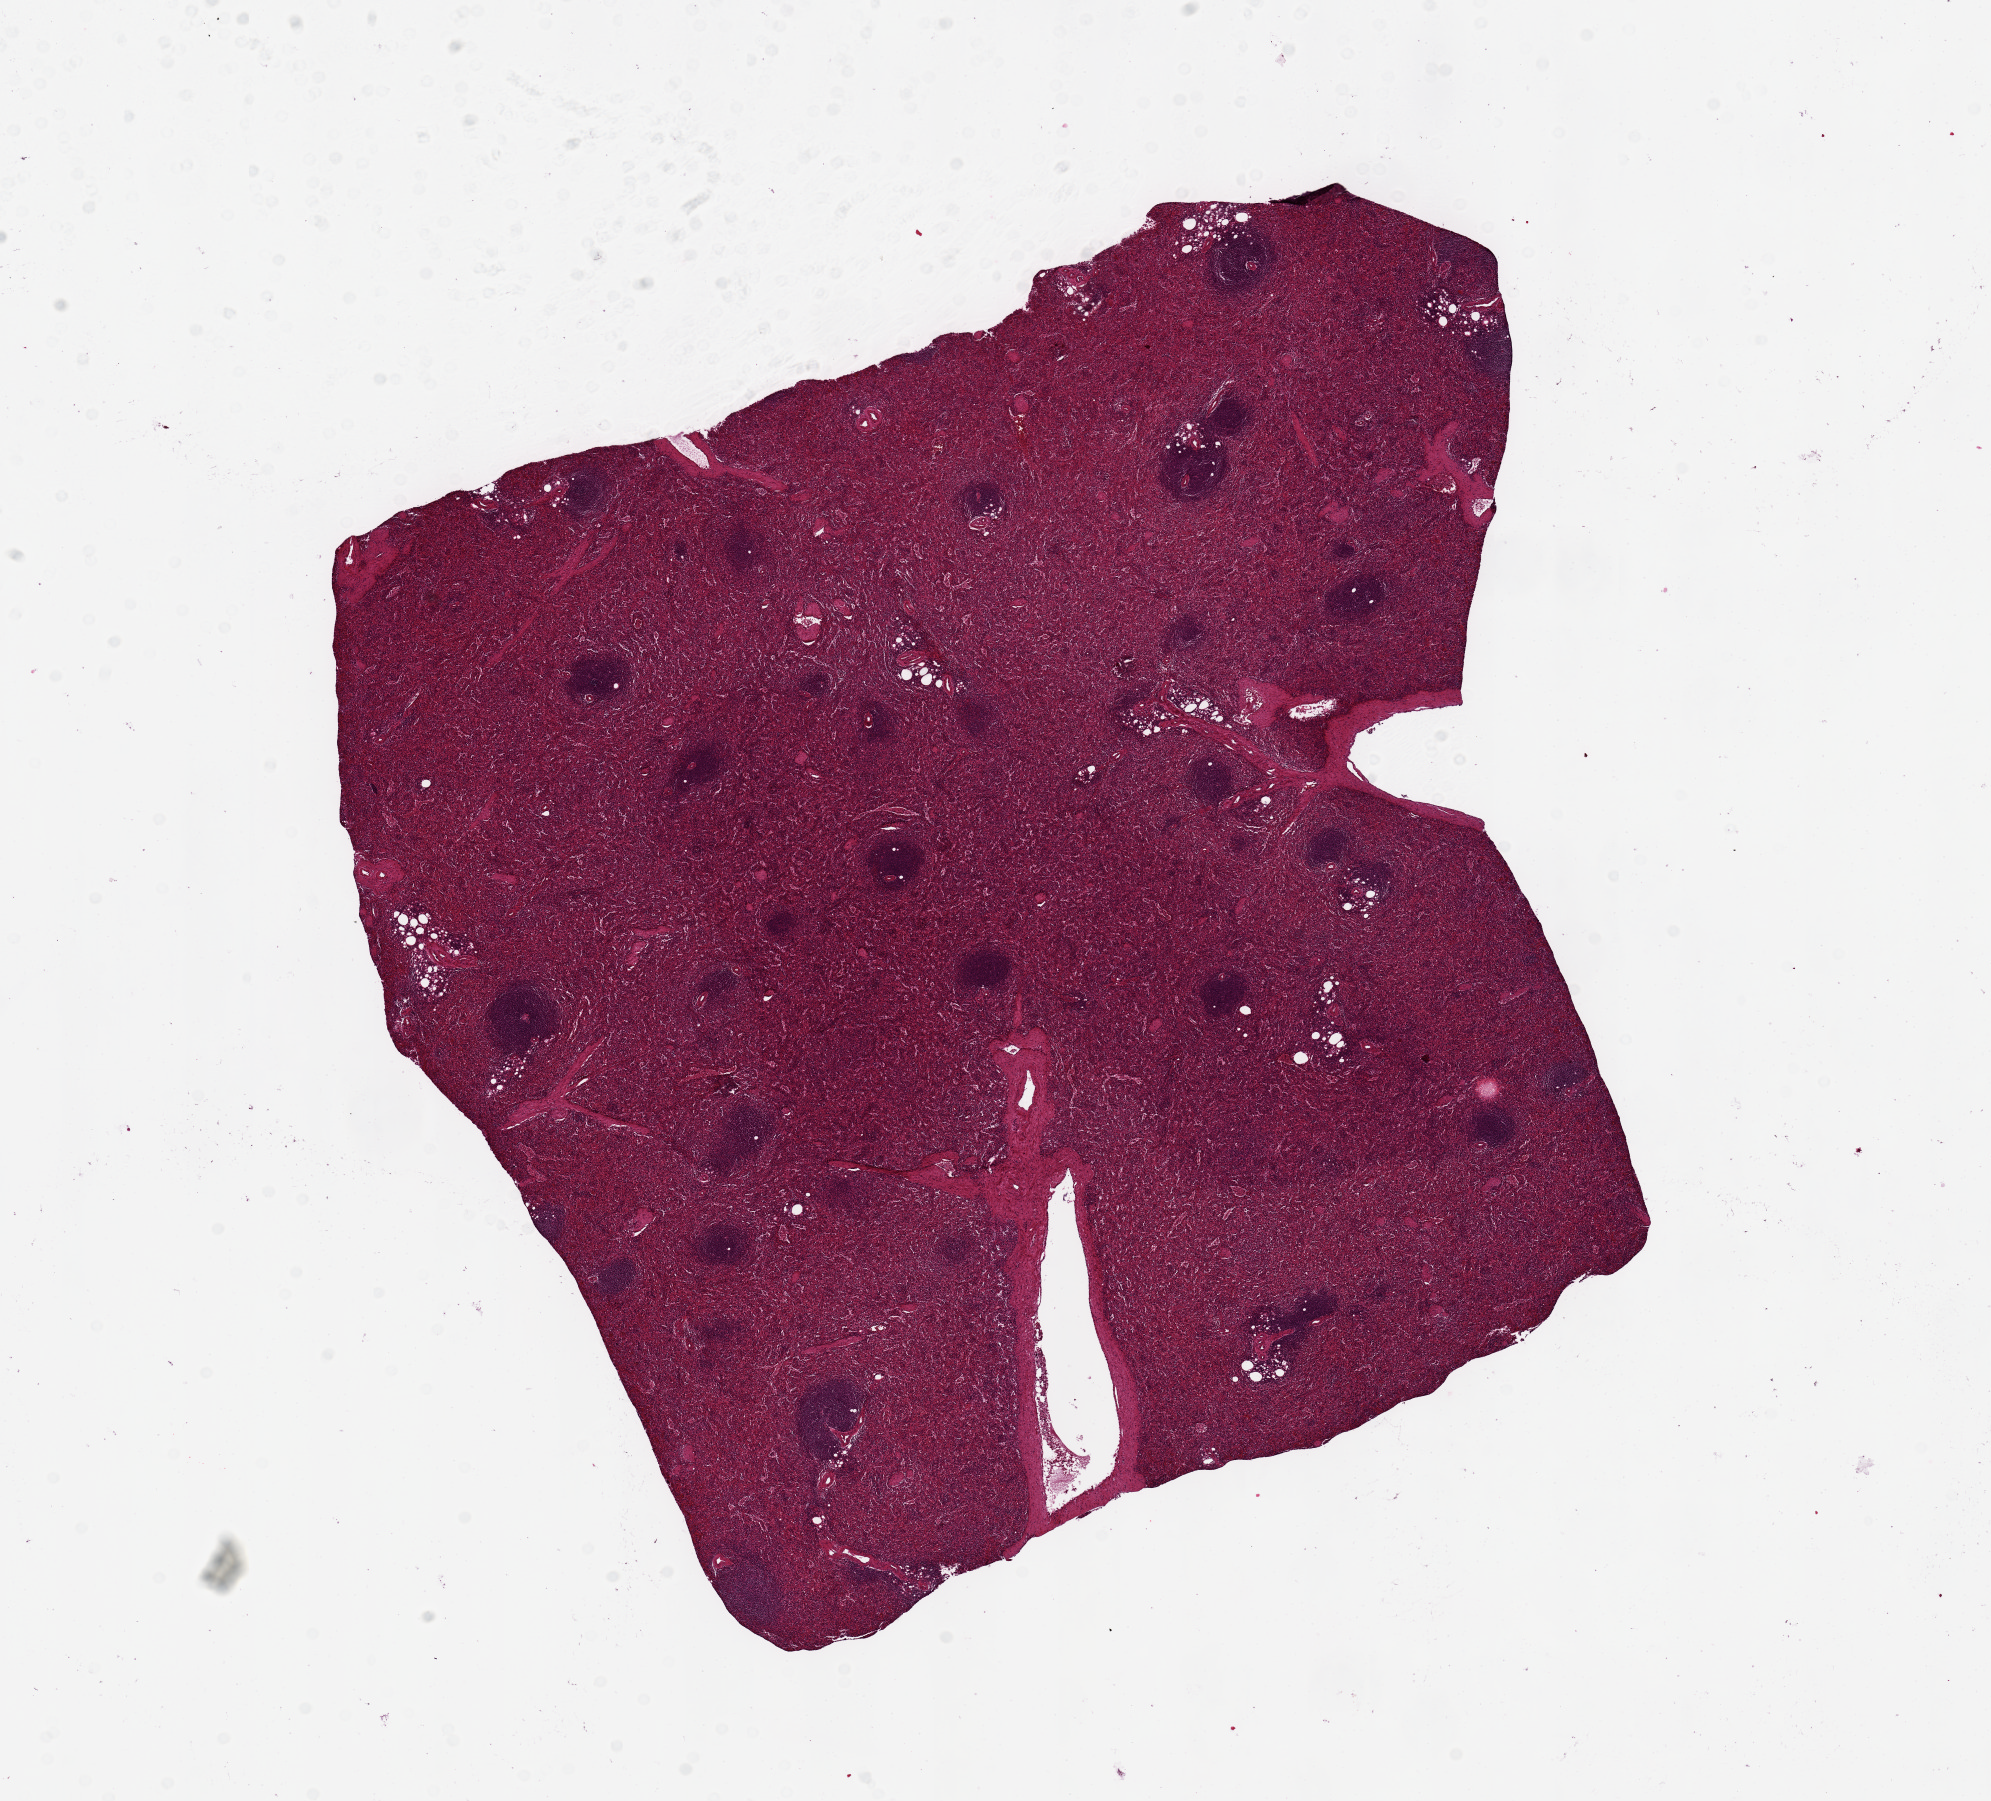
Digitized H&E-stained section, brightfield, shown as a low-resolution overview of the whole scanned area (about 15.8 x 14.2 mm, acquisition: 20x scan); PAXgene-fixed paraffin-embedded (PFPE) section; sampled site (target tissue): spleen; donor tissue sample. Donor: female.
Reviewer comment on this tissue sample: 9x7mm, areas of under-fixation.